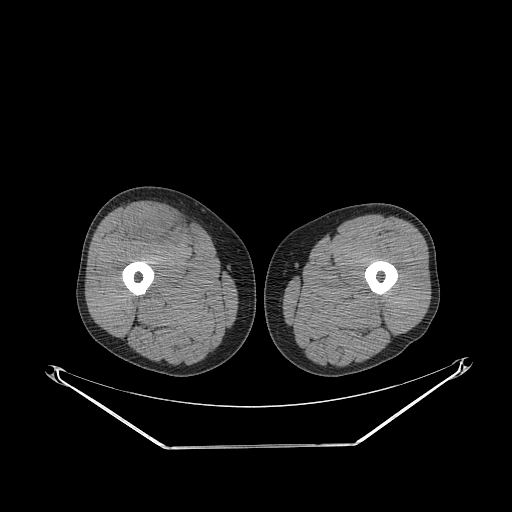
CT of an extremity soft-tissue mass (from a PET/CT study), one axial slice. Reconstruction kernel STANDARD. 140 kVp. Soft-tissue window (W 400 / L 40 HU). 512 × 512 image matrix. Male patient. Case-level facts recorded for this patient, not image findings: histological type: pleiomorphic leiomyosarcoma; grade: intermediate; site of the primary tumour: right thigh.
Outlined on this slice (expert contour drawn on MRI and transferred to this co-registered scan by the dataset authors):
- gross tumour volume including surrounding oedema: box from (x=126, y=206) to (x=181, y=245) px
- gross tumour volume (mass): (x=137, y=214)–(x=177, y=241)